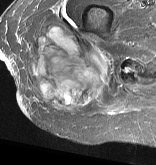
MRI of an extremity soft-tissue mass, one axial slice. Position 20 of 57 along the scan axis. STIR. MR volume resampled by the dataset authors to the PET/CT grid (not the native acquisition matrix). 156 × 165 image matrix, field of view 152 × 161 mm. Female patient. From the clinical record (not read from this slice): histological type: epithelioid sarcoma with vascular differentiation; site of the primary tumour: right buttock.
Outlined on this slice (expert contour drawn on MRI and transferred to this co-registered scan by the dataset authors):
- gross tumour volume (mass): box from (x=26, y=23) to (x=112, y=111) px